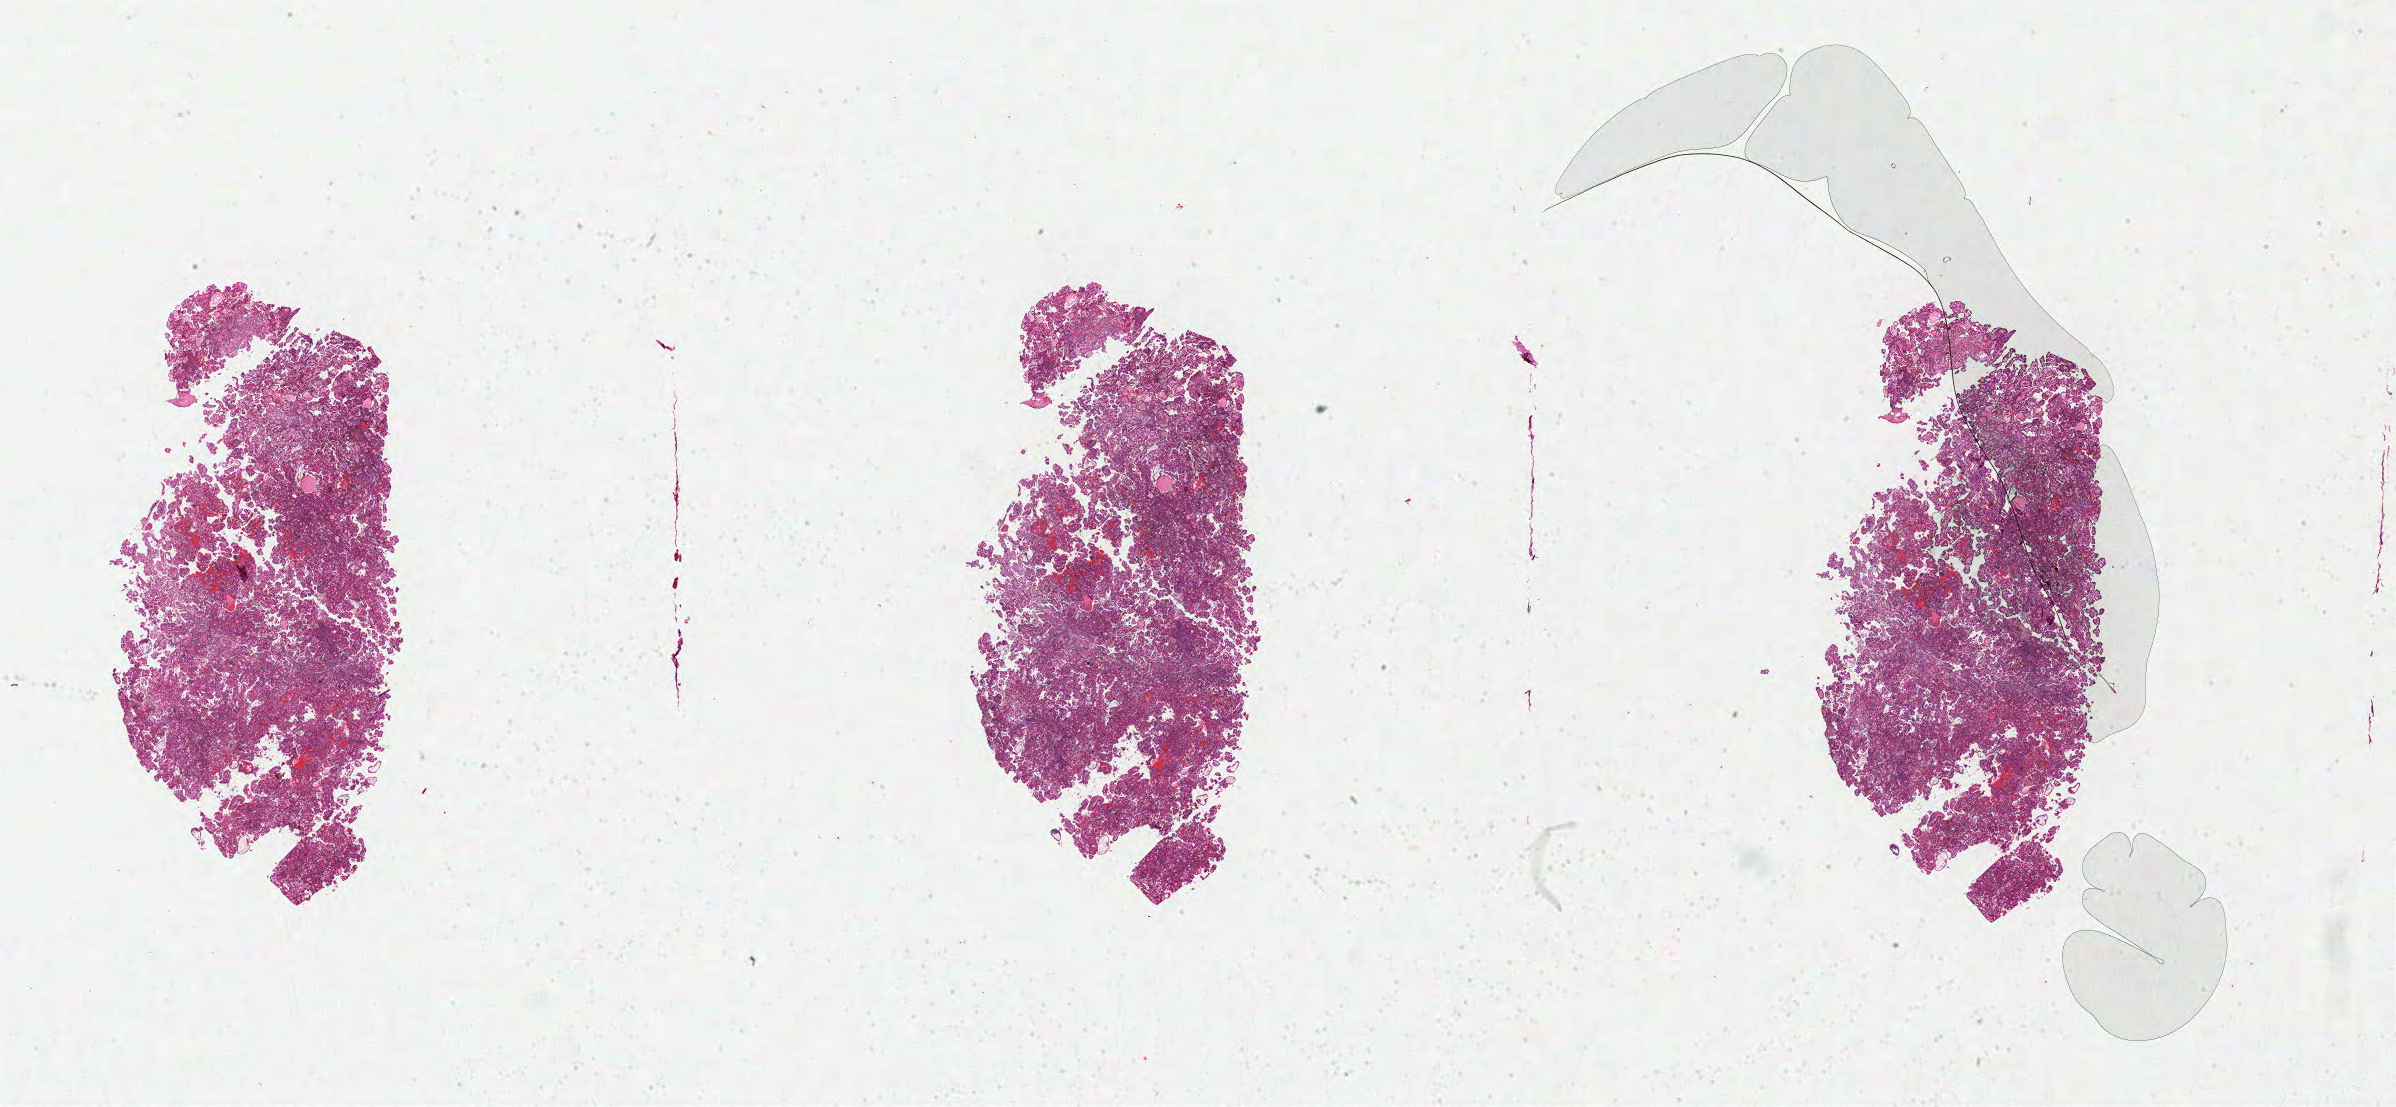
H&E whole-slide image, low-resolution overview of the scanned area, about 37.7 x 17.4 mm; formalin-fixed paraffin-embedded (FFPE) diagnostic section; sample: primary tumour, kidney. Male, age 51 years at initial diagnosis.
- pathologic diagnosis: Papillary adenocarcinoma, NOS